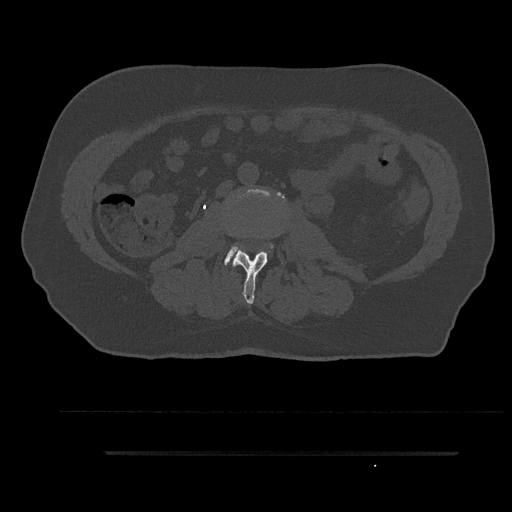
CT including the spine, one axial slice; position 79 of 797 along the scan axis; 120 kVp; bone window (W 1800 / L 400 HU); 0.5 mm slice thickness; 512 × 512 image matrix, field of view 432 × 432 mm. Patient: male, 63 years. Case-level facts recorded for this patient, not image findings: primary cancer: renal; vertebrae with lytic lesions (as recorded): T8.
Annotated regions visible in this slice (semi-automatically segmented with operator editing):
- L2 vertebra: box from (x=232, y=236) to (x=268, y=305) px
- L3 vertebra: (x=225, y=192)–(x=282, y=265)